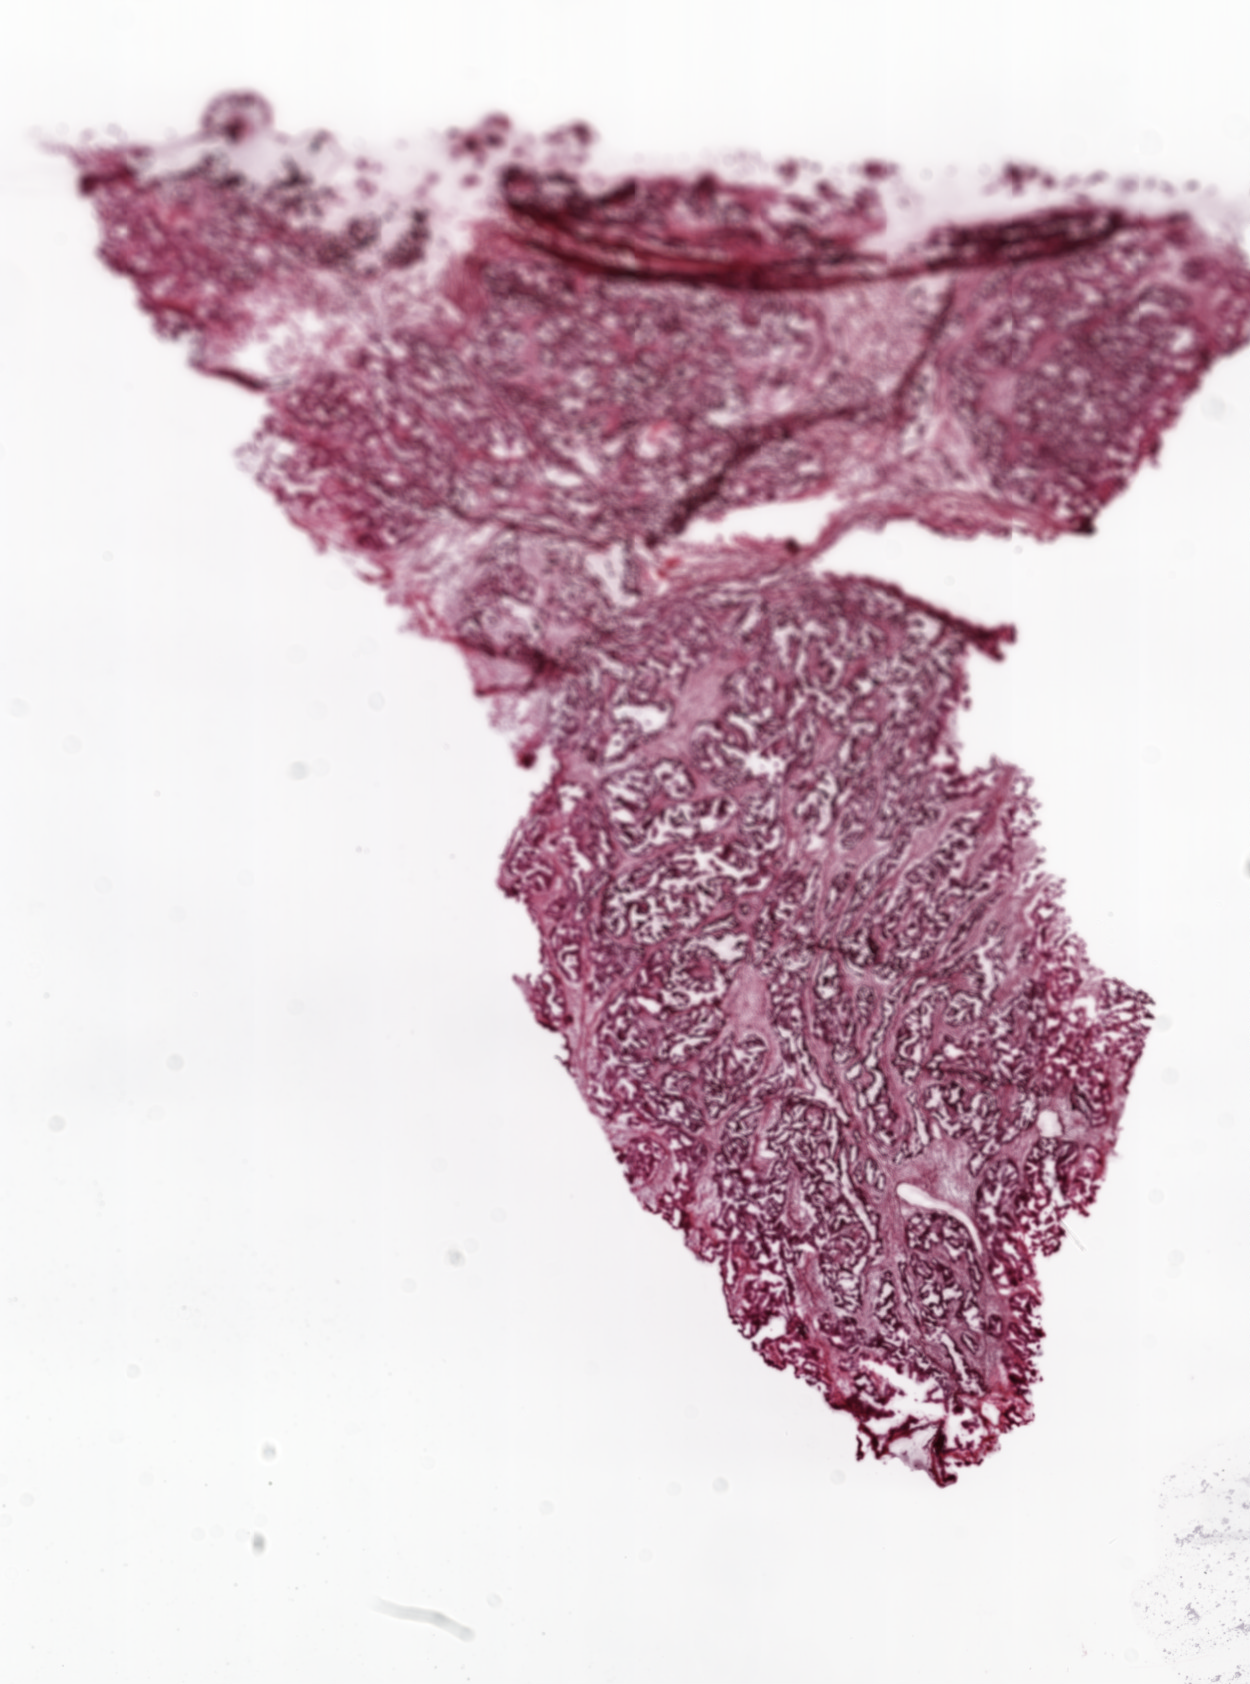
Hematoxylin and eosin (H&E) stained whole-slide image, a low-resolution overview of the entire scanned area, about 10.0 x 13.5 mm (from a 20x scan); frozen section; primary tumour sample from the ovary. Female patient; age at initial diagnosis 51 years. Histologic grade: G3 (poorly differentiated). Composition of this section per pathologist review: tumour cells 95%, tumour nuclei 85%, normal cells 0%, stromal cells 5%, necrosis 0%. Inflammatory infiltration, as recorded: lymphocyte infiltration 0%, monocyte infiltration 0%, neutrophil infiltration 0%.
Laterality: bilateral. Pathologic diagnosis: Serous cystadenocarcinoma, NOS. FIGO stage: IV.